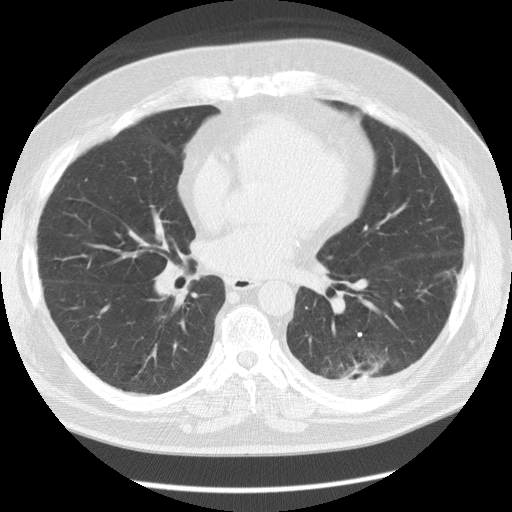
Low-dose screening chest CT, one axial slice; slice 62 of 126 in the series (ordered by position); 120 kVp; lung window (W 1500 / L -600 HU); 2.5 mm slice thickness; 512 × 512 image matrix, field of view 370 × 370 mm.
Structures marked on this image (expert manual segmentation):
- lesion 1 (tumor, lower lobe of left lung): bounding box [x1, y1, x2, y2] px = [346, 361, 377, 378]